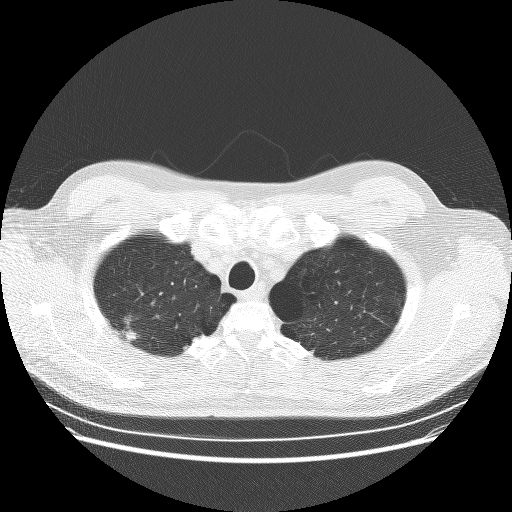
Low-dose screening chest CT, one axial slice; position 228 of 253 along the scan axis; lung window (W 1500 / L -600 HU); 512 × 512 image matrix.
Annotated regions visible in this slice (outlined manually by an expert reader):
- lesion 1 (tumor, upper lobe of right lung): bounding box (x1, y1, x2, y2) in pixels: (123, 330, 138, 341)